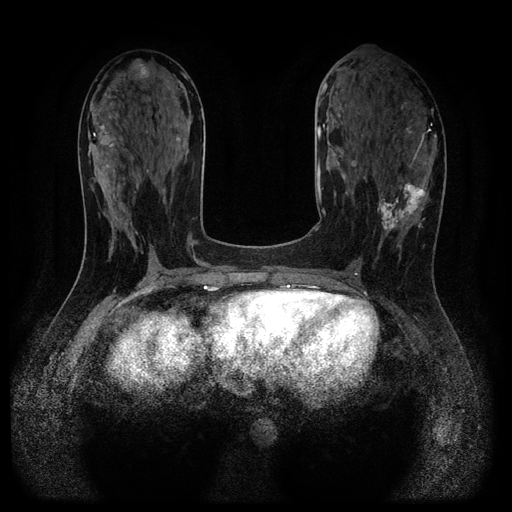
Breast MRI (dynamic contrast-enhanced, multi-phase), one axial slice; slice 50 of 116 in the series (ordered by position); dynamic contrast-enhanced series, time point 2 of 5 at this slice position (early post-contrast); 1.5 T; TE 2.7 ms, TR 5.4 ms; 512 × 512 image matrix, field of view 330 × 330 mm. Patient: female, 43 years.
Structures marked on this image (semi-automatically segmented with operator editing):
- breast lesion (labelled 'tumour' in the annotation; benign lesions carry a separate 'benign' label): bounding box <377,182,429,236> (left, top, right, bottom; pixels)
- breast lesion (labelled benign in the annotation): <120,59,150,81>